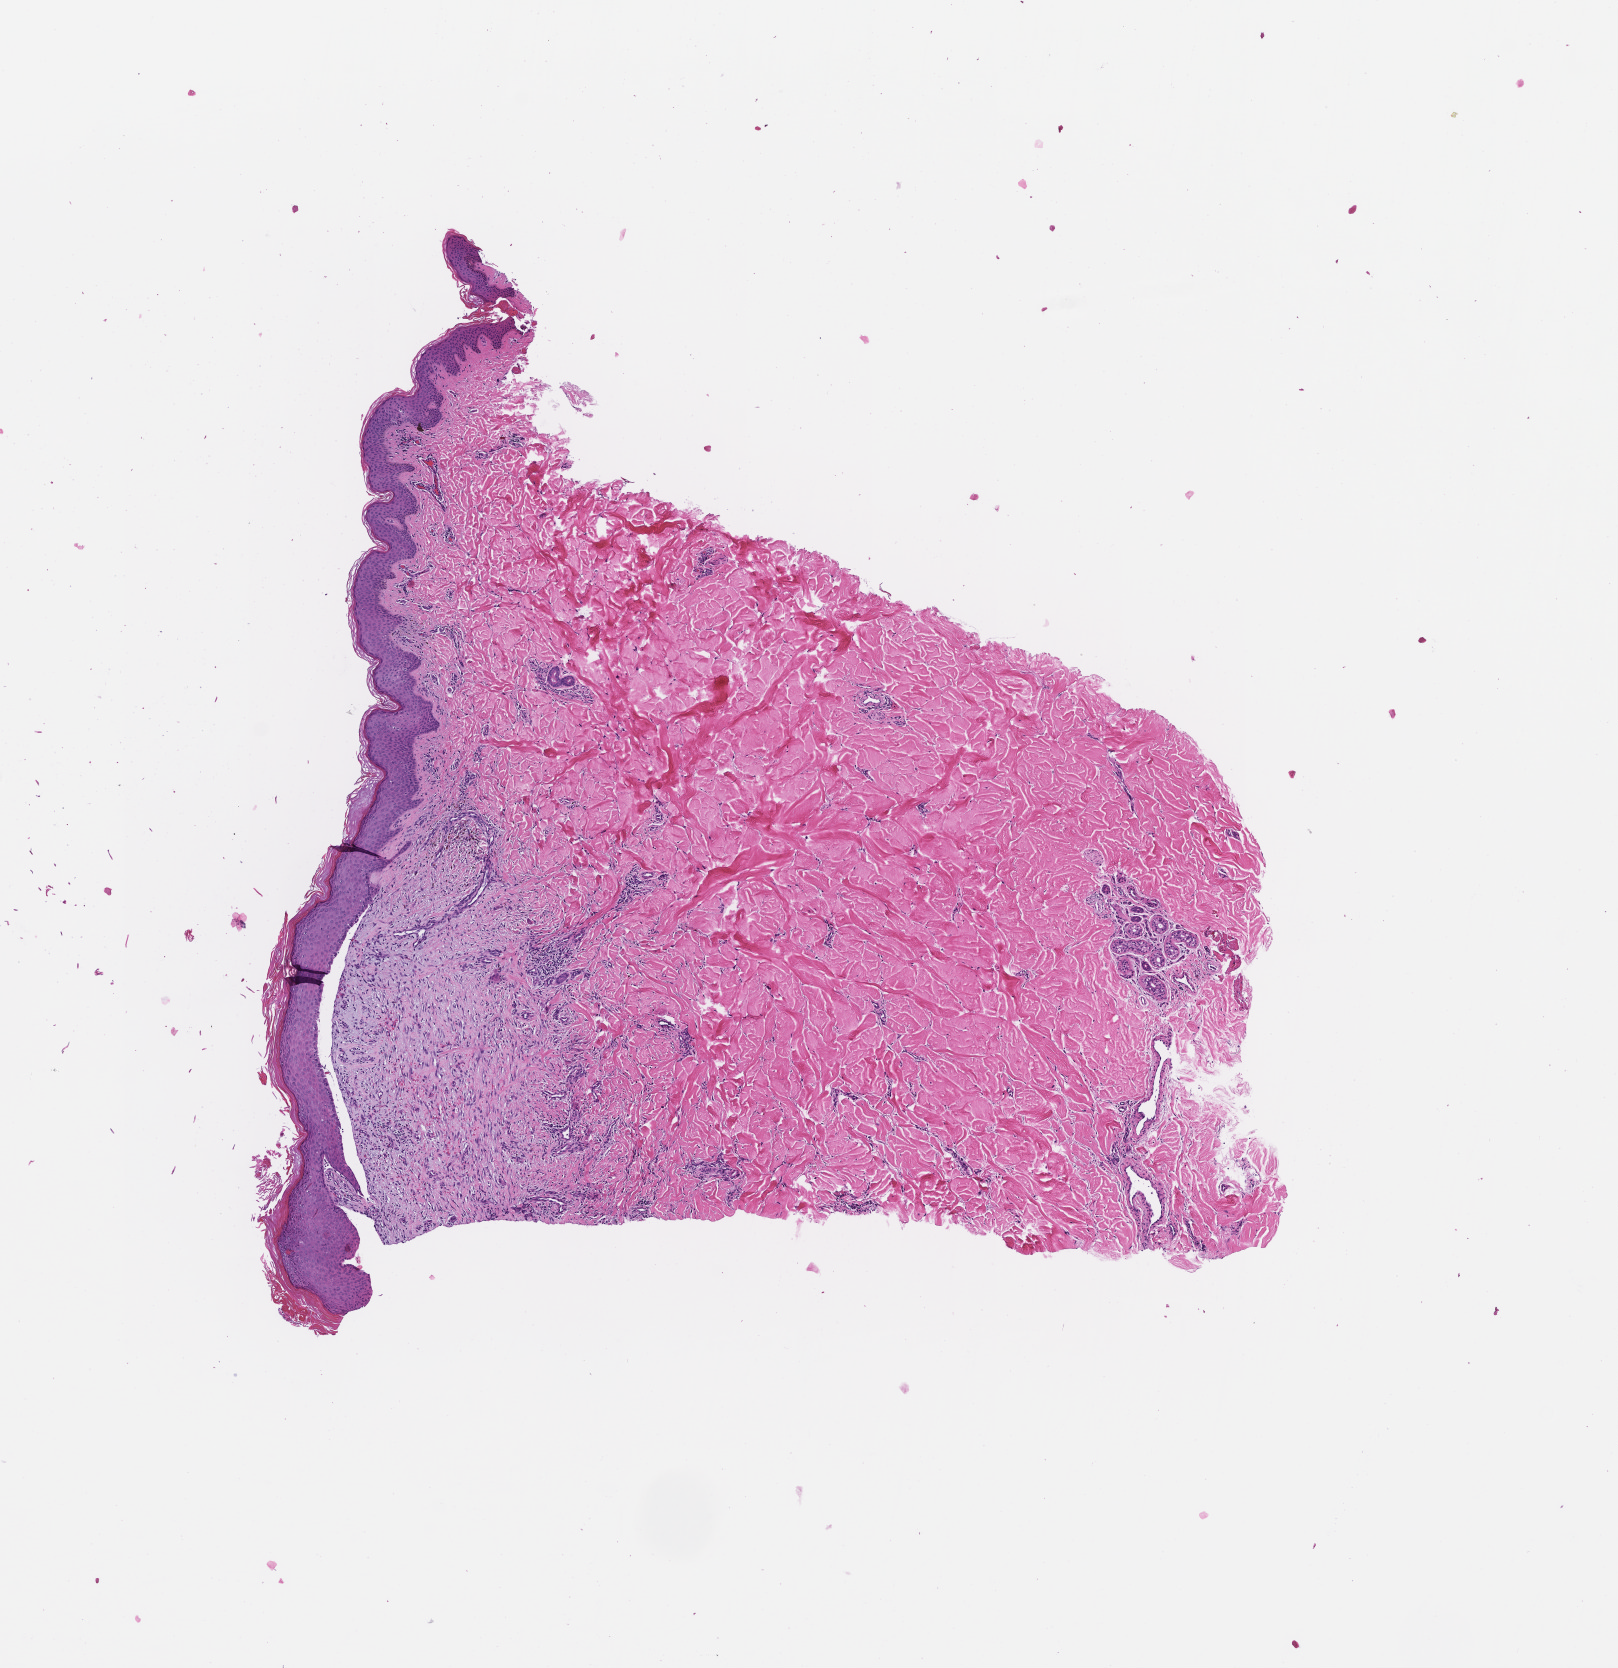
Whole-slide image, haematoxylin and eosin stain, low-resolution overview of the scanned area, about 6.5 x 6.7 mm, formalin-fixed, paraffin-embedded (FFPE) tissue, tissue site: skin, collected at baseline (before treatment). Patient: male.
This section: primary tumour tissue. Diagnosis: Melanoma.